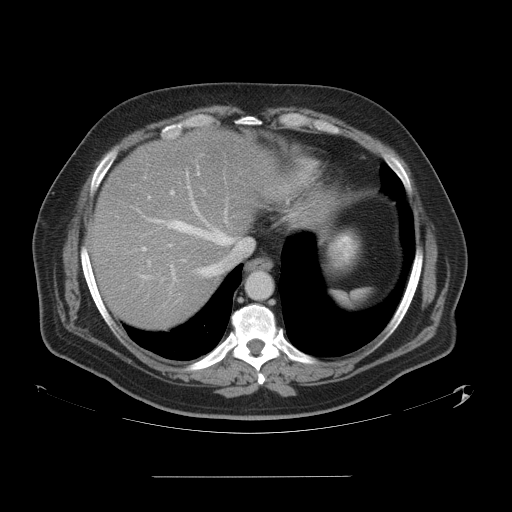
Contrast-enhanced abdominal CT, one axial slice. Slice 47 of 58 in the series (ordered by position). 120 kVp. Intravenous contrast given. Soft-tissue window (W 400 / L 40 HU). 5 mm slice thickness. 512 × 512 image matrix. Male patient, age 63 years. From the clinical record (not read from this slice): diagnosis: colorectal cancer liver metastases, imaged before liver resection; multiple liver metastases: no; largest metastasis: 4.2 cm; disease in both lobes: no.
Outlined on this slice (manually delineated by an expert):
- hepatic veins: bounding box <138,172,246,303> (left, top, right, bottom; pixels)
- liver: <93,130,276,328>
- planned liver remnant (the part of the liver to remain after resection): <93,203,226,329>
- portal vein (with intrahepatic branches): <139,173,200,278>